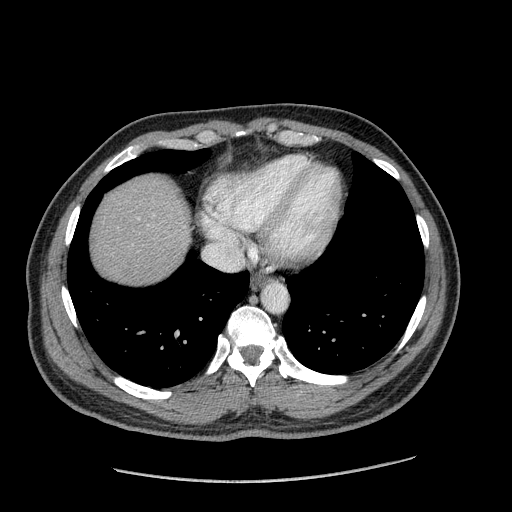
Contrast-enhanced abdominal CT (liver protocol), one axial slice; position 165 of 182 along the scan axis; soft-tissue window (W 400 / L 40 HU); 512 × 512 image matrix. From the clinical record (not read from this slice): diagnosis: hepatocellular carcinoma (patient treated with transarterial chemoembolisation; whether this scan precedes or follows treatment is not stated here); TNM stage (as recorded): Stage-I; Child-Pugh class: A; tumour differentiation: well differentiated; tumour nodularity: uninodular.
Annotated regions visible in this slice (semi-automatic segmentation, software-assisted and operator-edited):
- abdominal aorta: bounding box <261,284,287,313> (left, top, right, bottom; pixels)
- liver parenchyma outside the tumour (the mass and vessels are separate outlines, so this box may not span the whole liver): <92,176,190,284>